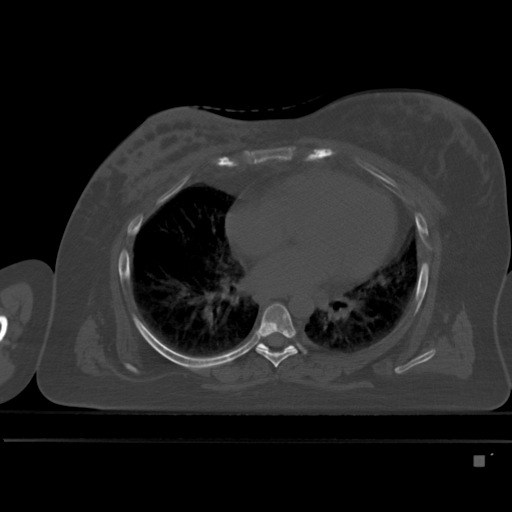
CT including the spine, one axial slice; position 302 of 495 along the scan axis; bone window (W 1800 / L 400 HU); 1.5 mm slice thickness; 512 × 512 image matrix, field of view 404 × 404 mm. Patient: female, 33 years. From the clinical record (not read from this slice): primary cancer: breast.
Outlined on this slice (semi-automatically segmented with operator editing):
- T6 vertebra: bounding box [x1, y1, x2, y2] px = [256, 303, 298, 368]
- T7 vertebra: [257, 343, 296, 350]